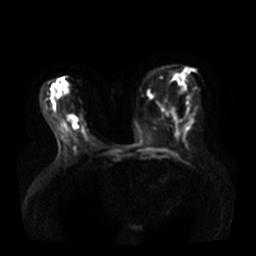
Breast MRI, one axial slice. Position 16 of 36 along the scan axis. Diffusion-weighted series; image 2 of 4 stored at this slice position (different b-values; order by instance number). 3 T. 5 mm slice thickness. 256 × 256 image matrix. Female patient.
Annotated regions visible in this slice (expert manual segmentation):
- tumour on diffusion-weighted imaging: bounding box [x1, y1, x2, y2] px = [70, 116, 77, 123]